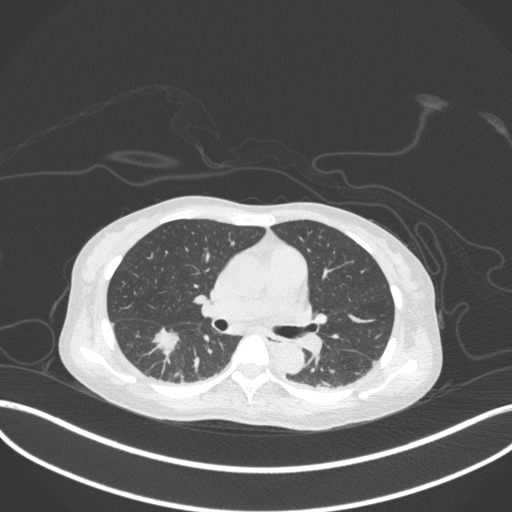
Chest CT, one axial slice. Slice 175 of 260 in the series (ordered by position). Reconstruction kernel B31f. 120 kVp. Lung window (W 1500 / L -600 HU). 1 mm slice thickness. 512 × 512 image matrix, field of view 400 × 400 mm. Patient: female, 44 years. Case-level facts recorded for this patient, not image findings: clinical TNM (as recorded): T1c N0 M0.
Structures marked on this image (bounding box drawn by a radiologist):
- lung tumour (recorded histology: adenocarcinoma): box from (x=148, y=321) to (x=181, y=364) px